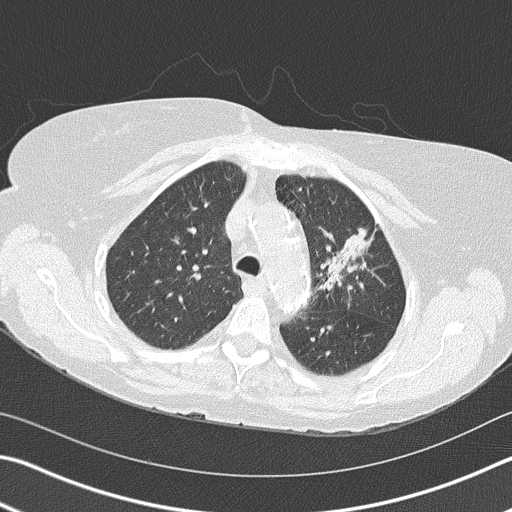
Axial slice from a low-dose chest CT screening exam. Second annual screen. Lung window (W 1500 / L -600 HU). Lung (sharp) reconstruction kernel (B50f). Female participant, aged 68 years at enrolment.
Expert reader's lesion annotation, bounding box (x1, y1, x2, y2) in pixels: (293, 206, 388, 314). Screening reader's record for this exam (one nodule recorded; not confirmed to be the boxed lesion): non-calcified nodule or mass ≥4 mm, left upper lobe, 4 × 2 mm, spiculated (stellate) margins, soft tissue attenuation, pre-existing on the prior screen: yes; interval growth: yes. Official screen result: positive, other. Lung cancer was diagnosed 392 days after this screen (after the third annual screen): adenocarcinoma, NOS, left upper lobe, poorly differentiated (G3), stage IB (AJCC 6th edition), 50 mm at pathology.